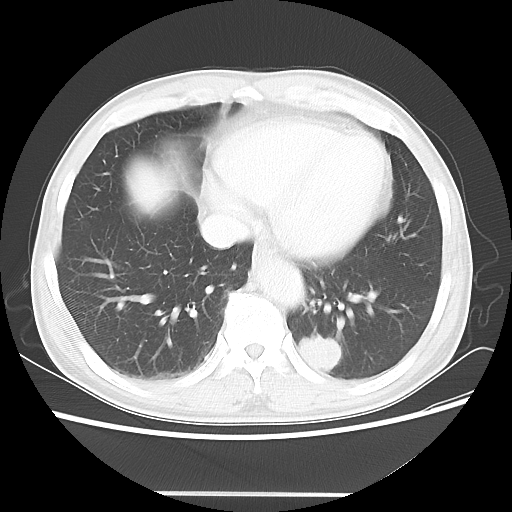
Chest CT, one axial slice. Position 17 of 60 along the scan axis. Lung window (W 1500 / L -600 HU). 5 mm slice thickness. 512 × 512 image matrix. Male patient, age 55 years. From the clinical record (not read from this slice): clinical TNM (as recorded): T1c N3 M0.
Annotated regions visible in this slice (rectangle marked by the reading radiologist):
- lung tumour (recorded histology: small cell carcinoma): bounding box <291,328,351,383> (left, top, right, bottom; pixels)